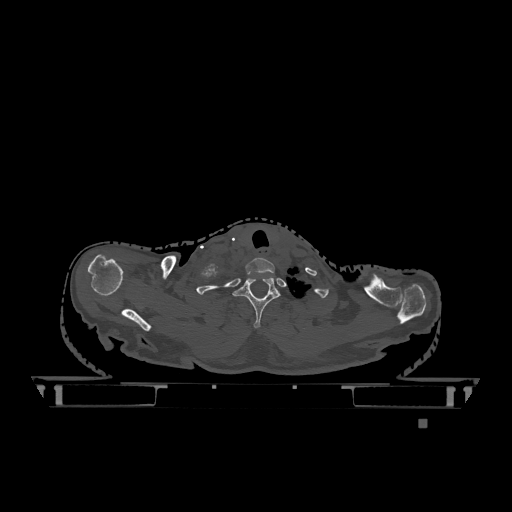
CT including the spine, one axial slice. Position 1000 of 1317 along the scan axis. Bone window (W 1800 / L 400 HU). 0.5 mm slice thickness. 512 × 512 image matrix, field of view 500 × 500 mm. Patient: female, 74 years. From the clinical record (not read from this slice): primary cancer: lung; vertebrae with lytic lesions (as recorded): T1, T4, T5, T6, L4, L5.
Annotated regions visible in this slice (semi-automatic segmentation, software-assisted and operator-edited):
- T1 vertebra: bounding box <233,276,280,328> (left, top, right, bottom; pixels)